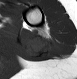
MRI of an extremity soft-tissue mass, one axial slice; MR volume resampled by the dataset authors to the PET/CT grid (not the native acquisition matrix); 3.27 mm slice thickness; 77 × 79 image matrix, field of view 75 × 77 mm. Female patient. From the clinical record (not read from this slice): histological type: malignant fibrous histiocytoma; grade: low; site of the primary tumour: left arm.
Outlined on this slice (expert contour drawn on MRI and transferred to this co-registered scan by the dataset authors):
- gross tumour volume (mass): bounding box (x1, y1, x2, y2) in pixels: (26, 29, 56, 58)